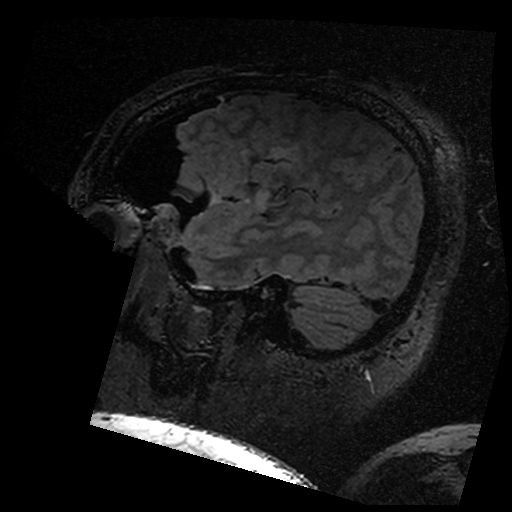
Brain MRI from a brain-tumour surgery series, one sagittal slice; position 134 of 176 along the scan axis; T2 FLAIR; 512 × 512 image matrix. From the clinical record (not read from this slice): histopathology: Astrocytoma; WHO grade: 3; IDH mutation: yes; tumour location: Left Insular.
Annotated regions visible in this slice (outlined manually by an expert reader):
- residual tumour: bounding box (x1, y1, x2, y2) in pixels: (282, 158, 286, 163)